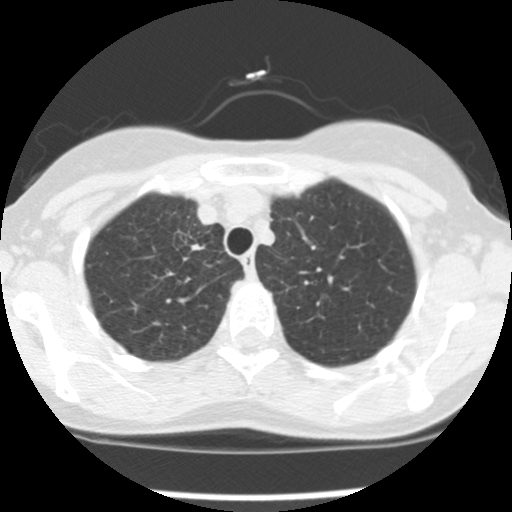
Low-dose screening chest CT, one axial slice. Position 124 of 157 along the scan axis. 120 kVp. Lung window (W 1500 / L -600 HU). 2.5 mm slice thickness. 512 × 512 image matrix, field of view 282 × 282 mm.
Annotated regions visible in this slice (expert manual segmentation):
- lesion 1 (tumor, upper lobe of right lung): box from (x=191, y=244) to (x=205, y=251) px